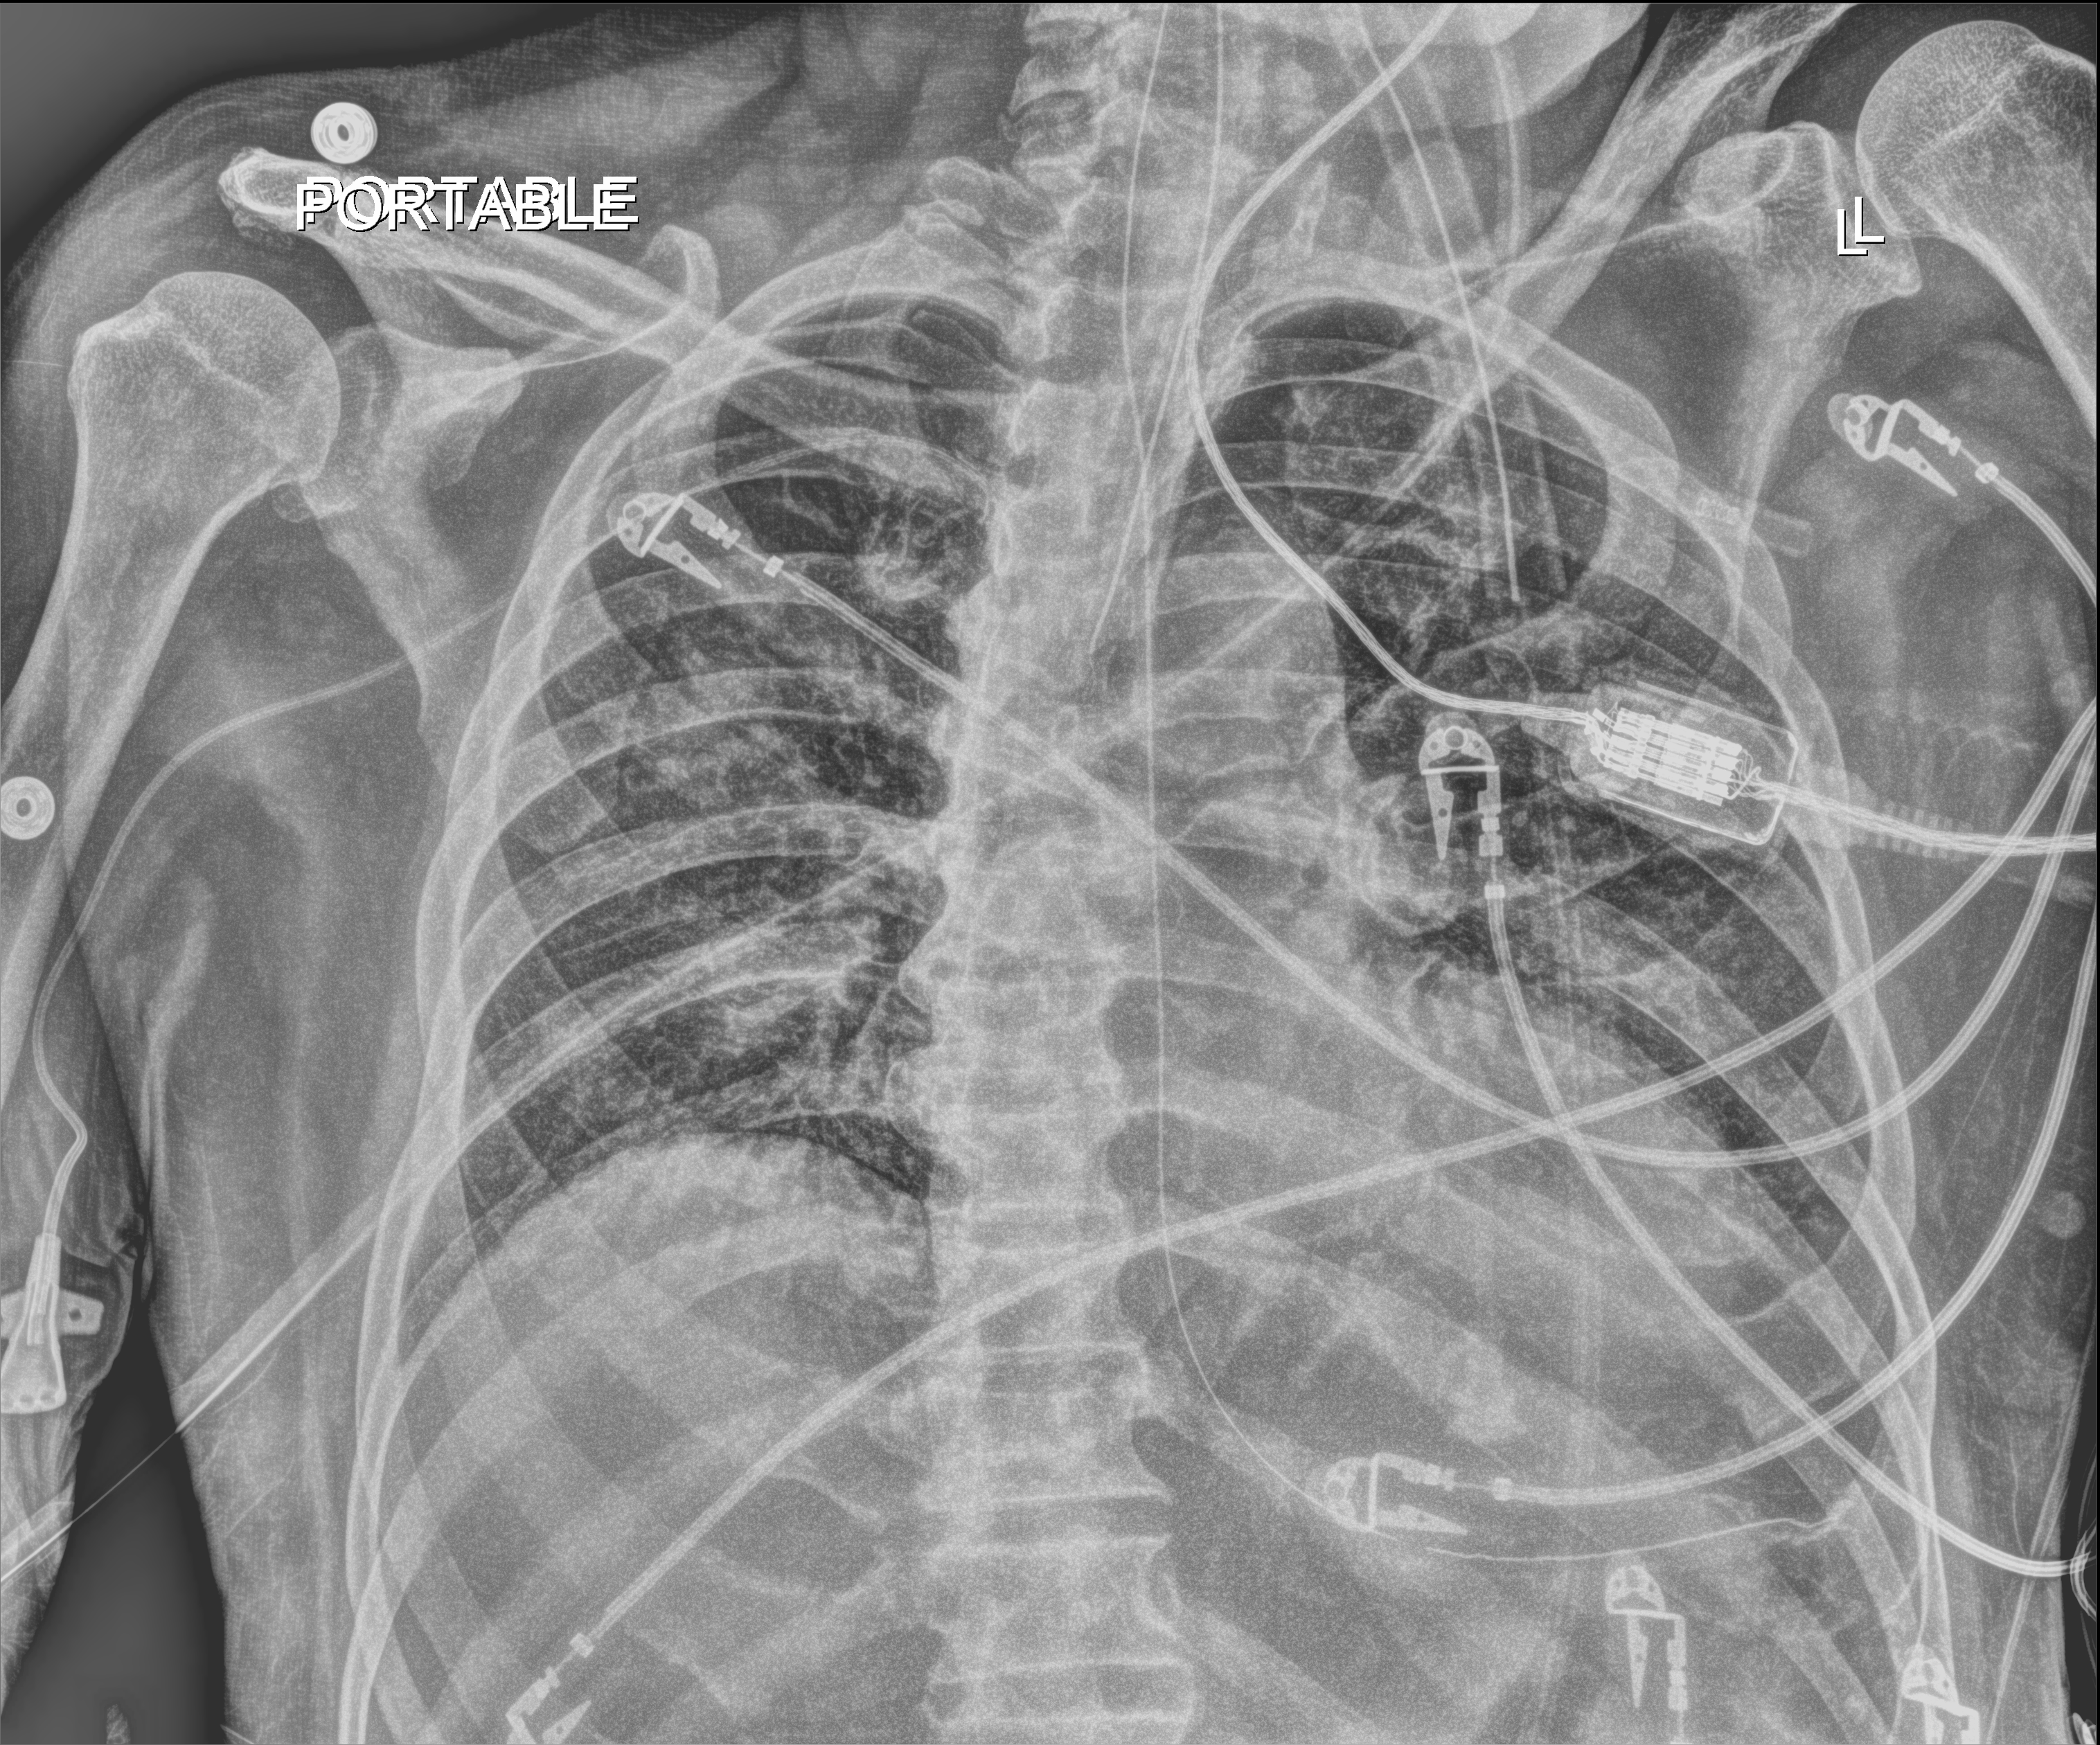
Bedside chest radiograph (digital radiography); anteroposterior (AP) projection. Patient hospitalised with COVID-19; male, aged 75–90 years.
From the hospital-stay record, not from the radiograph (when in the stay this image was taken is not recorded): mechanically ventilated during this hospital stay: yes.